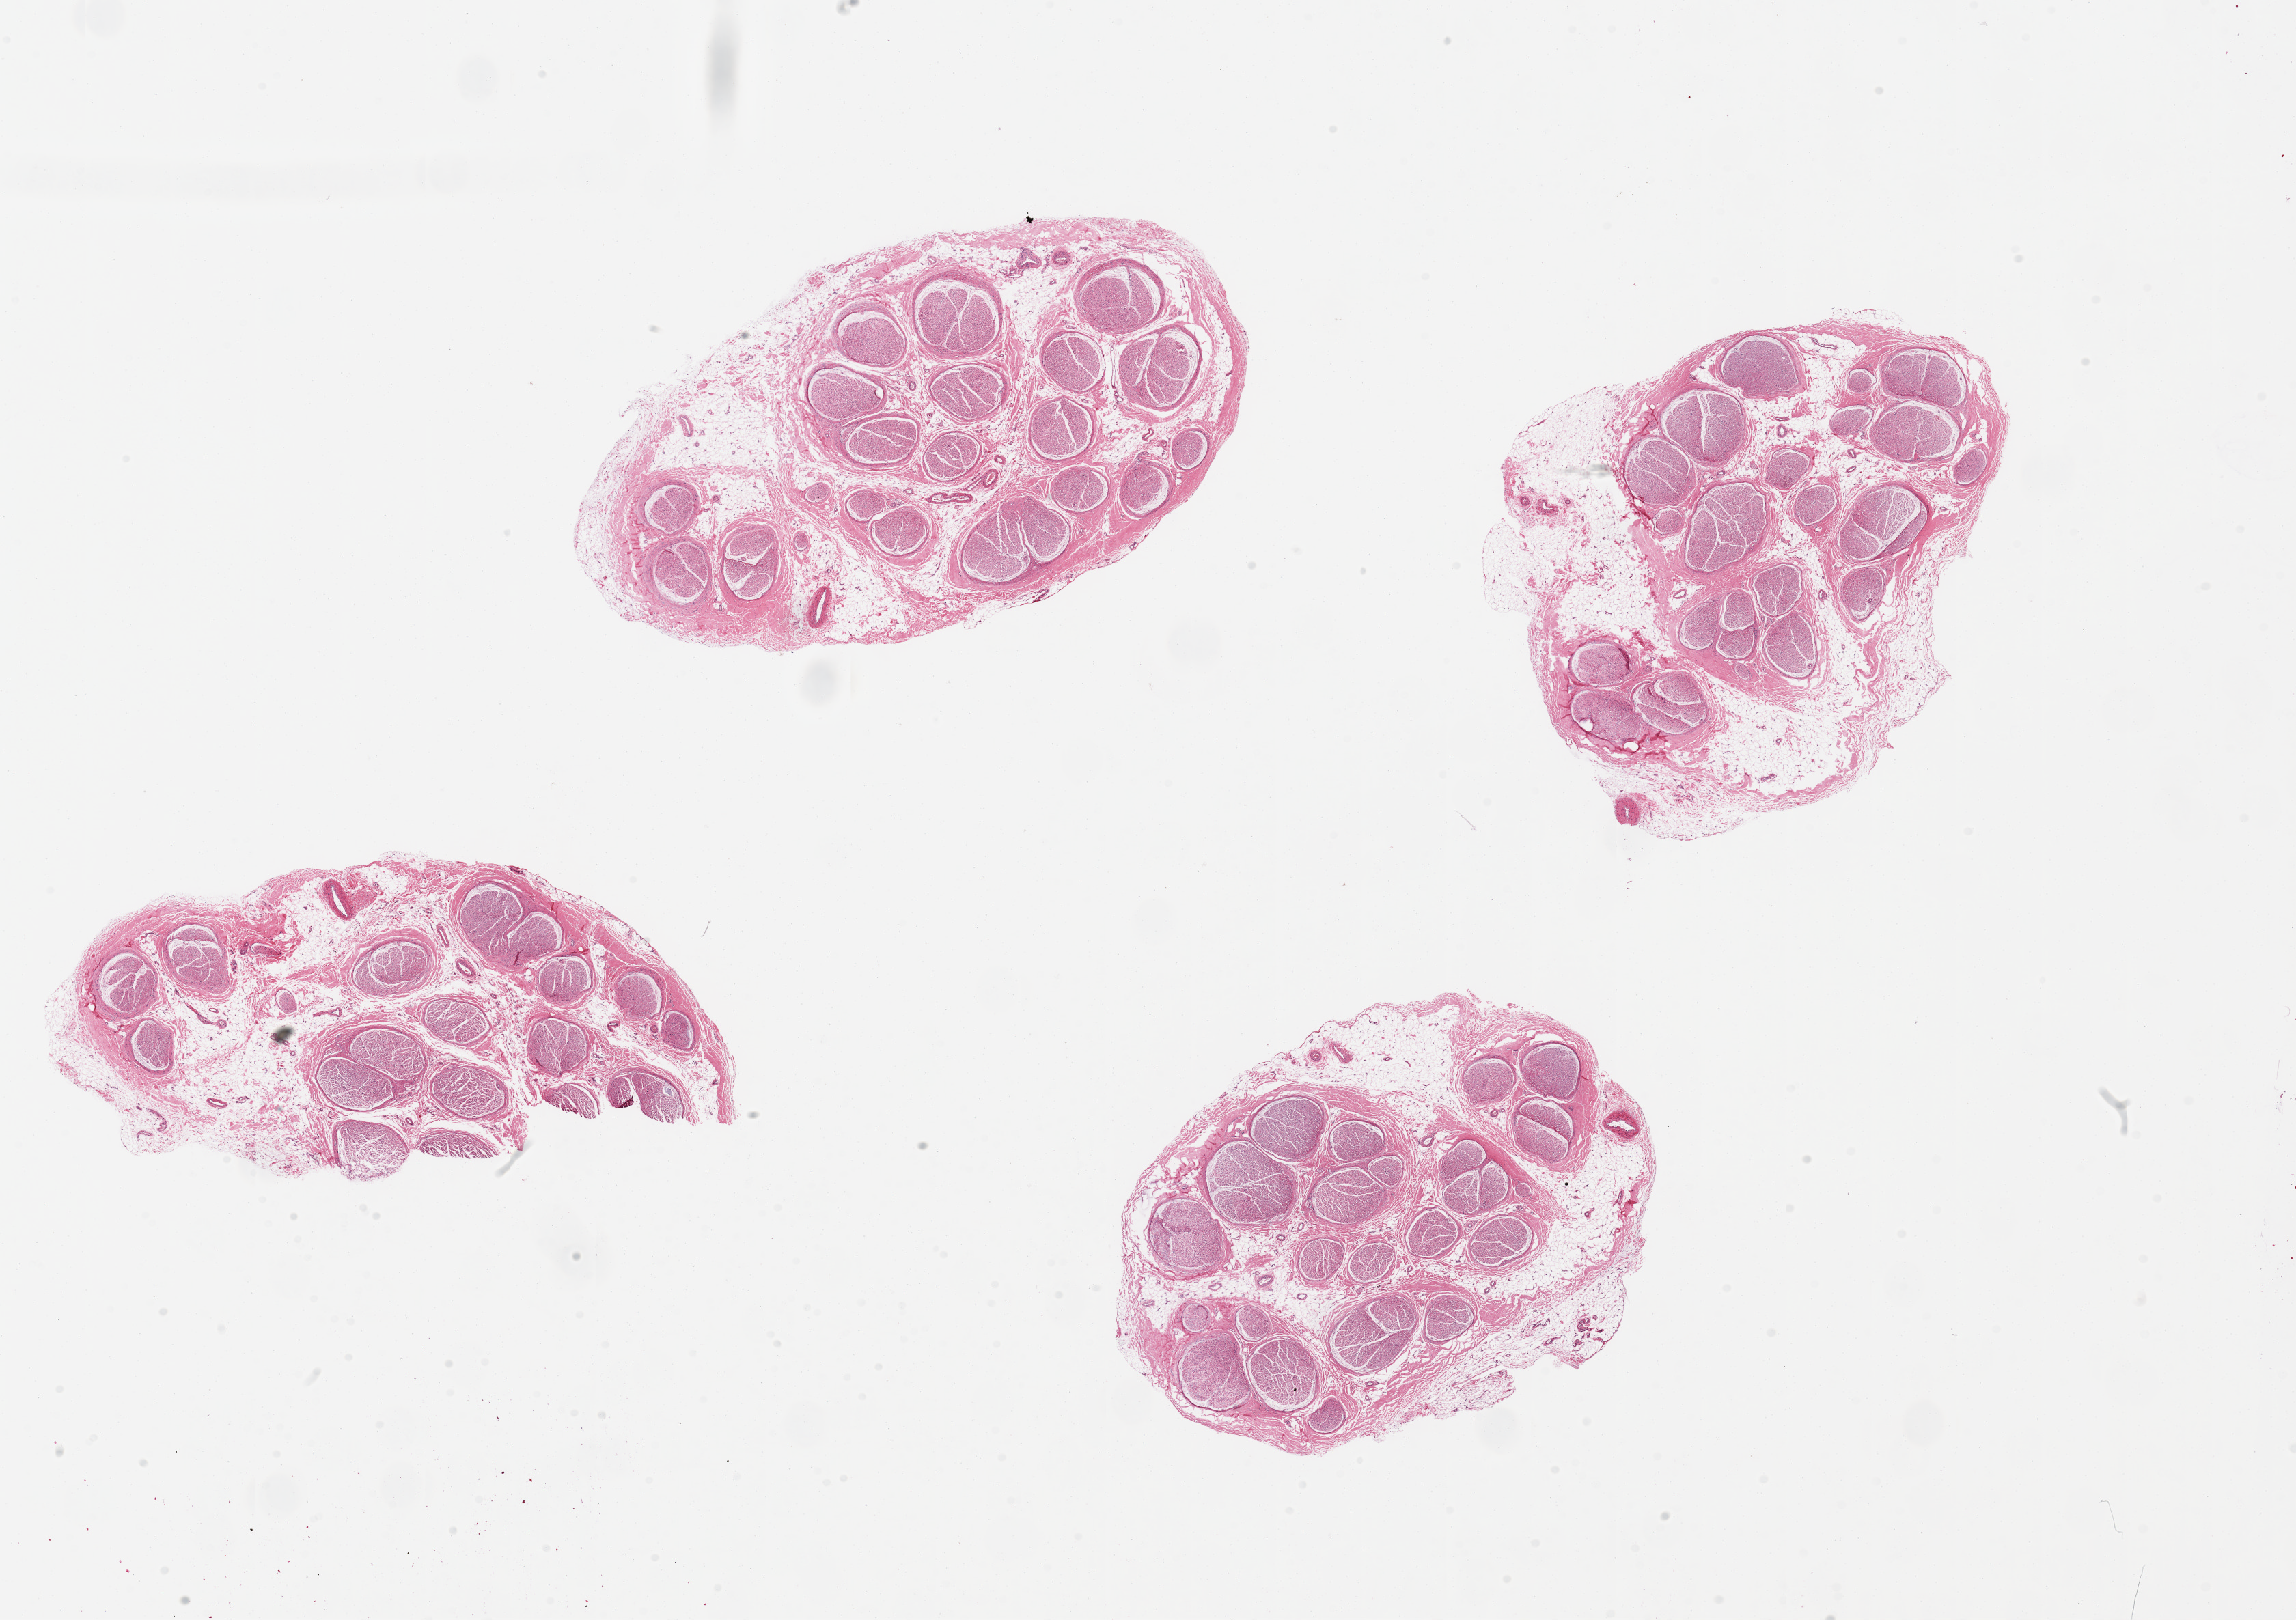
H&E whole-slide image, whole scanned area (about 26.6 x 18.8 mm, acquisition: 20x scan) shown as a low-resolution overview; PAXgene-fixed paraffin-embedded (PFPE) section; section of tibial nerve (target tissue); donor tissue sample. Donor: male.
- reviewer comment on this tissue sample: 4 pieces, nubbins of adherent fat up to ~1mm